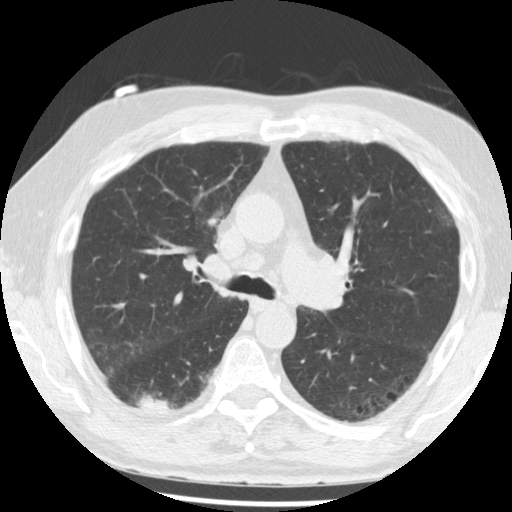
Low-dose screening chest CT, one axial slice. Slice 135 of 221 in the series (ordered by position). 120 kVp. Lung window (W 1500 / L -600 HU). 2.5 mm slice thickness. 512 × 512 image matrix.
Outlined on this slice (outlined manually by an expert reader):
- lesion 1 (tumor, lower lobe of right lung): box from (x=137, y=396) to (x=175, y=411) px